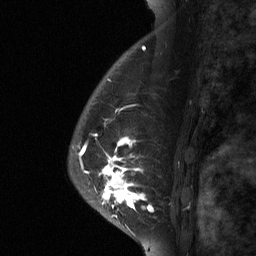
Breast MRI (dynamic contrast-enhanced), one sagittal slice; slice 48 of 64 in the series (ordered by position); dynamic contrast-enhanced study with each time point stored as its own series, time point 2 of 3 at this slice position (early post-contrast, ordered by acquisition time); 1.5 T; TE 4.8 ms, TR 27 ms; 2 mm slice thickness; 256 × 256 image matrix. Patient: female, 56 years. Case-level facts recorded for this patient, not image findings: setting: breast cancer imaged before/during neoadjuvant chemotherapy; receptor status: HER2-positive.
Annotated regions visible in this slice (semi-automatically segmented with operator editing):
- analysis volume of interest (the breast-tissue region the enhancement analysis was run in; not a lesion): bounding box [x1, y1, x2, y2] px = [94, 104, 182, 229]
- tumour enhancement mask (voxels above the 90 % enhancement threshold inside the analysis volume of interest): [99, 136, 154, 212]